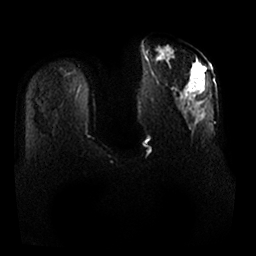
Breast MRI, one axial slice. Position 8 of 25 along the scan axis. Diffusion-weighted series; image 2 of 4 stored at this slice position (different b-values; order by instance number). 1.5 T. 4 mm slice thickness. 256 × 256 image matrix. Female patient.
Outlined on this slice (expert manual segmentation):
- tumour on diffusion-weighted imaging: bounding box [x1, y1, x2, y2] px = [157, 47, 205, 89]